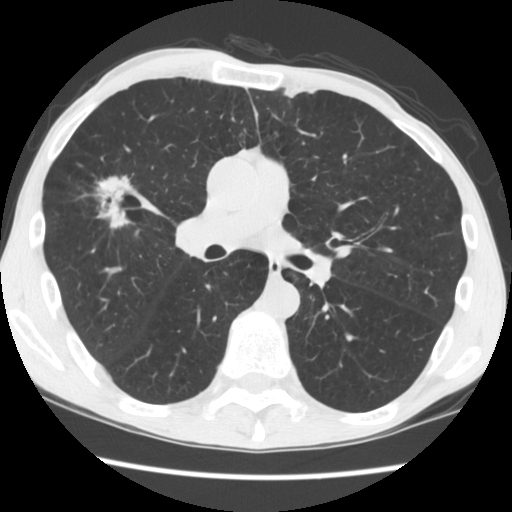
Low-dose screening chest CT, one axial slice; slice 98 of 181 in the series (ordered by position); reconstruction kernel STANDARD; lung window (W 1500 / L -600 HU); 2.5 mm slice thickness; 512 × 512 image matrix, field of view 330 × 330 mm.
Structures marked on this image (manually delineated by an expert):
- lesion 1 (tumor, upper lobe of right lung): box from (x=94, y=176) to (x=131, y=229) px